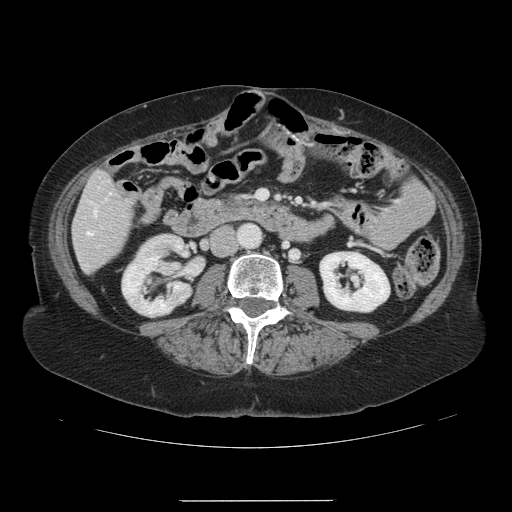
Contrast-enhanced abdominal CT, one axial slice. Position 30 of 141 along the scan axis. 120 kVp. Intravenous contrast given. Soft-tissue window (W 400 / L 40 HU). 2.5 mm slice thickness. 512 × 512 image matrix. Female patient, age 74 years. From the clinical record (not read from this slice): diagnosis: colorectal cancer liver metastases, imaged before liver resection; multiple liver metastases: yes; largest metastasis: 7 cm.
Annotated regions visible in this slice (outlined manually by an expert reader):
- hepatic veins: bounding box <87,210,96,235> (left, top, right, bottom; pixels)
- liver: <74,173,133,272>
- planned liver remnant (the part of the liver to remain after resection): <77,197,96,272>